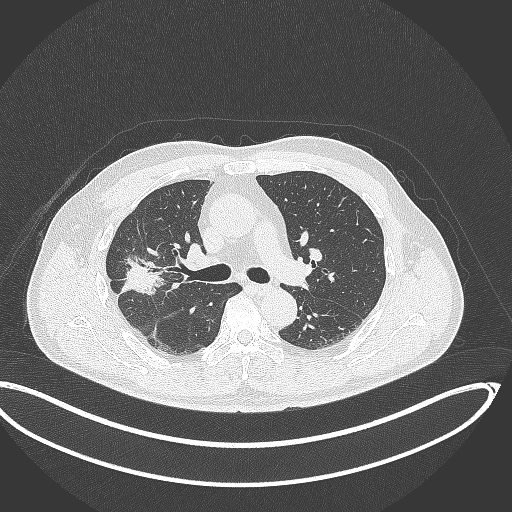
Chest CT, one axial slice; slice 213 of 391 in the series (ordered by position); reconstruction kernel B70f; lung window (W 1500 / L -600 HU); 512 × 512 image matrix, field of view 439 × 439 mm. Male patient, age 63 years. From the clinical record (not read from this slice): clinical TNM (as recorded): T1c N0 M0; histopathological grade: G2-3.
Annotated regions visible in this slice (bounding box drawn by a radiologist):
- lung tumour (recorded histology: adenocarcinoma): box from (x=118, y=248) to (x=169, y=299) px